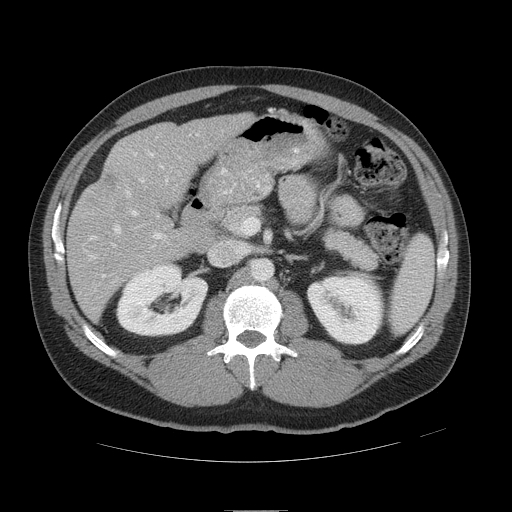
Contrast-enhanced abdominal CT, one axial slice; slice 25 of 49 in the series (ordered by position); 120 kVp; intravenous contrast given; soft-tissue window (W 400 / L 40 HU); 5 mm slice thickness; 512 × 512 image matrix, field of view 425 × 425 mm. Male patient, age 52 years. Case-level facts recorded for this patient, not image findings: diagnosis: colorectal cancer liver metastases, imaged before liver resection; multiple liver metastases: yes; largest metastasis: 5.1 cm; disease in both lobes: yes.
Outlined on this slice (outlined manually by an expert reader):
- hepatic veins: box from (x=114, y=153) to (x=167, y=248) px
- liver: (x=69, y=115)–(x=246, y=314)
- planned liver remnant (the part of the liver to remain after resection): (x=132, y=115)–(x=246, y=187)
- portal vein (with intrahepatic branches): (x=89, y=186)–(x=167, y=260)
- liver metastasis: (x=106, y=176)–(x=118, y=186)